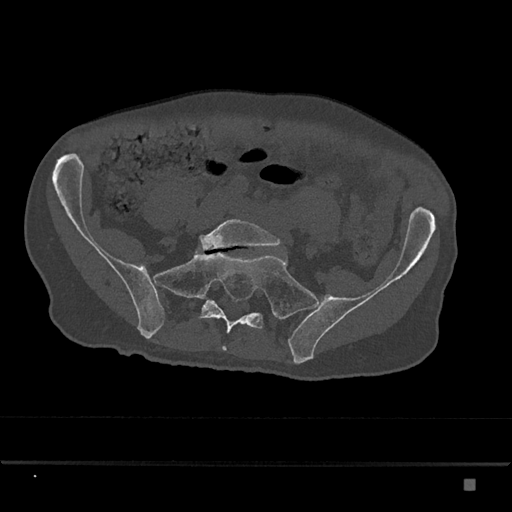
CT including the spine, one axial slice. Slice 227 of 797 in the series (ordered by position). Reconstruction kernel Br40s/3. 120 kVp. Bone window (W 1800 / L 400 HU). 512 × 512 image matrix. Male patient, age 72 years. From the clinical record (not read from this slice): primary cancer: prostate.
Outlined on this slice (semi-automatically segmented with operator editing):
- L5 vertebra: bounding box <199,219,281,250> (left, top, right, bottom; pixels)